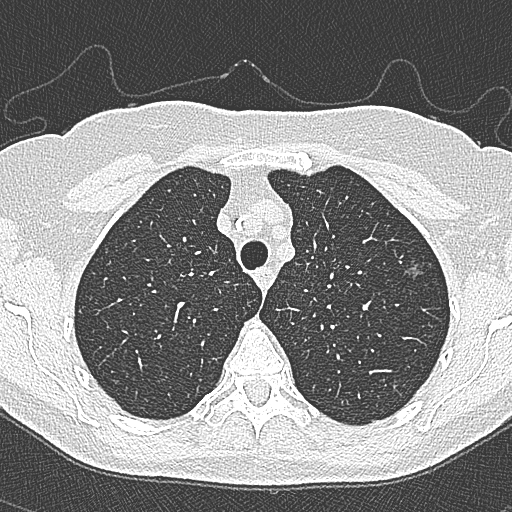
Low-dose screening chest CT, axial slice, second annual screen, lung window (W 1500 / L -600 HU), 1 mm slice thickness, 120 kVp, slice 67 of 350 in the series, 512 × 512 image matrix, field of view 298 × 298 mm. Female, age 65 years at enrolment.
Expert-annotated lung lesion, bounding box <396,251,432,284> (left, top, right, bottom; pixels). The screening reader recorded 4 non-calcified nodules or masses ≥4 mm on this exam; which of them this box marks is not recorded. Official screen result: positive, change unspecified: nodule(s) >= 4 mm or enlarging nodule(s), mass(es), or other non-specific abnormalities suspicious for lung cancer. Participant outcome: lung cancer diagnosed 54 days after this screen — bronchiolo-alveolar carcinoma, non-mucinous, left upper lobe, stage IA (AJCC 6th edition), 10 mm at pathology.